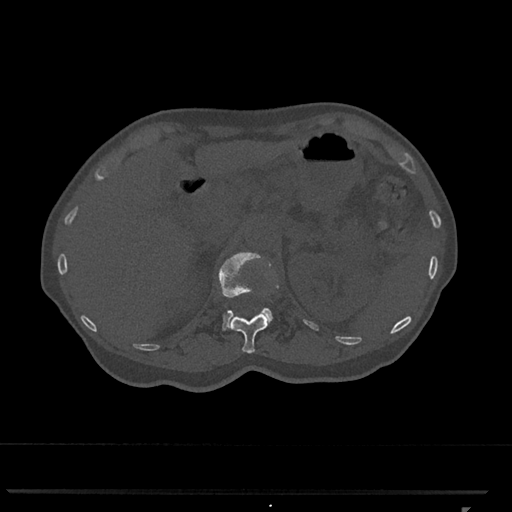
CT including the spine, one axial slice; position 438 of 793 along the scan axis; reconstruction kernel Br40s/3; 120 kVp; bone window (W 1800 / L 400 HU); 512 × 512 image matrix, field of view 380 × 380 mm. Female patient, age 62 years. From the clinical record (not read from this slice): primary cancer: renal.
Outlined on this slice (semi-automatic segmentation, software-assisted and operator-edited):
- L1 vertebra: bounding box <218,252,273,331> (left, top, right, bottom; pixels)
- T12 vertebra: <228,253,278,353>